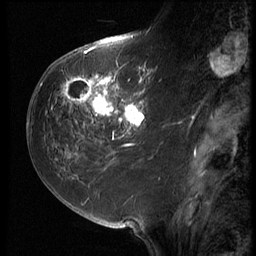
Breast MRI (dynamic contrast-enhanced), one sagittal slice. Slice 27 of 64 in the series (ordered by position). 3 images stored at this slice position (order not interpretable as contrast timing). 1.5 T. TE 4.2 ms, TR 9 ms. 256 × 256 image matrix, field of view 180 × 180 mm. Female patient, age 59 years. From the clinical record (not read from this slice): setting: breast cancer imaged before/during neoadjuvant chemotherapy; receptor status: HER2-positive.
Outlined on this slice (semi-automatic segmentation, software-assisted and operator-edited):
- analysis volume of interest (the breast-tissue region the enhancement analysis was run in; not a lesion): bounding box <54,65,155,132> (left, top, right, bottom; pixels)
- tumour enhancement mask (voxels above the 140 % enhancement threshold inside the analysis volume of interest): <61,65,146,132>